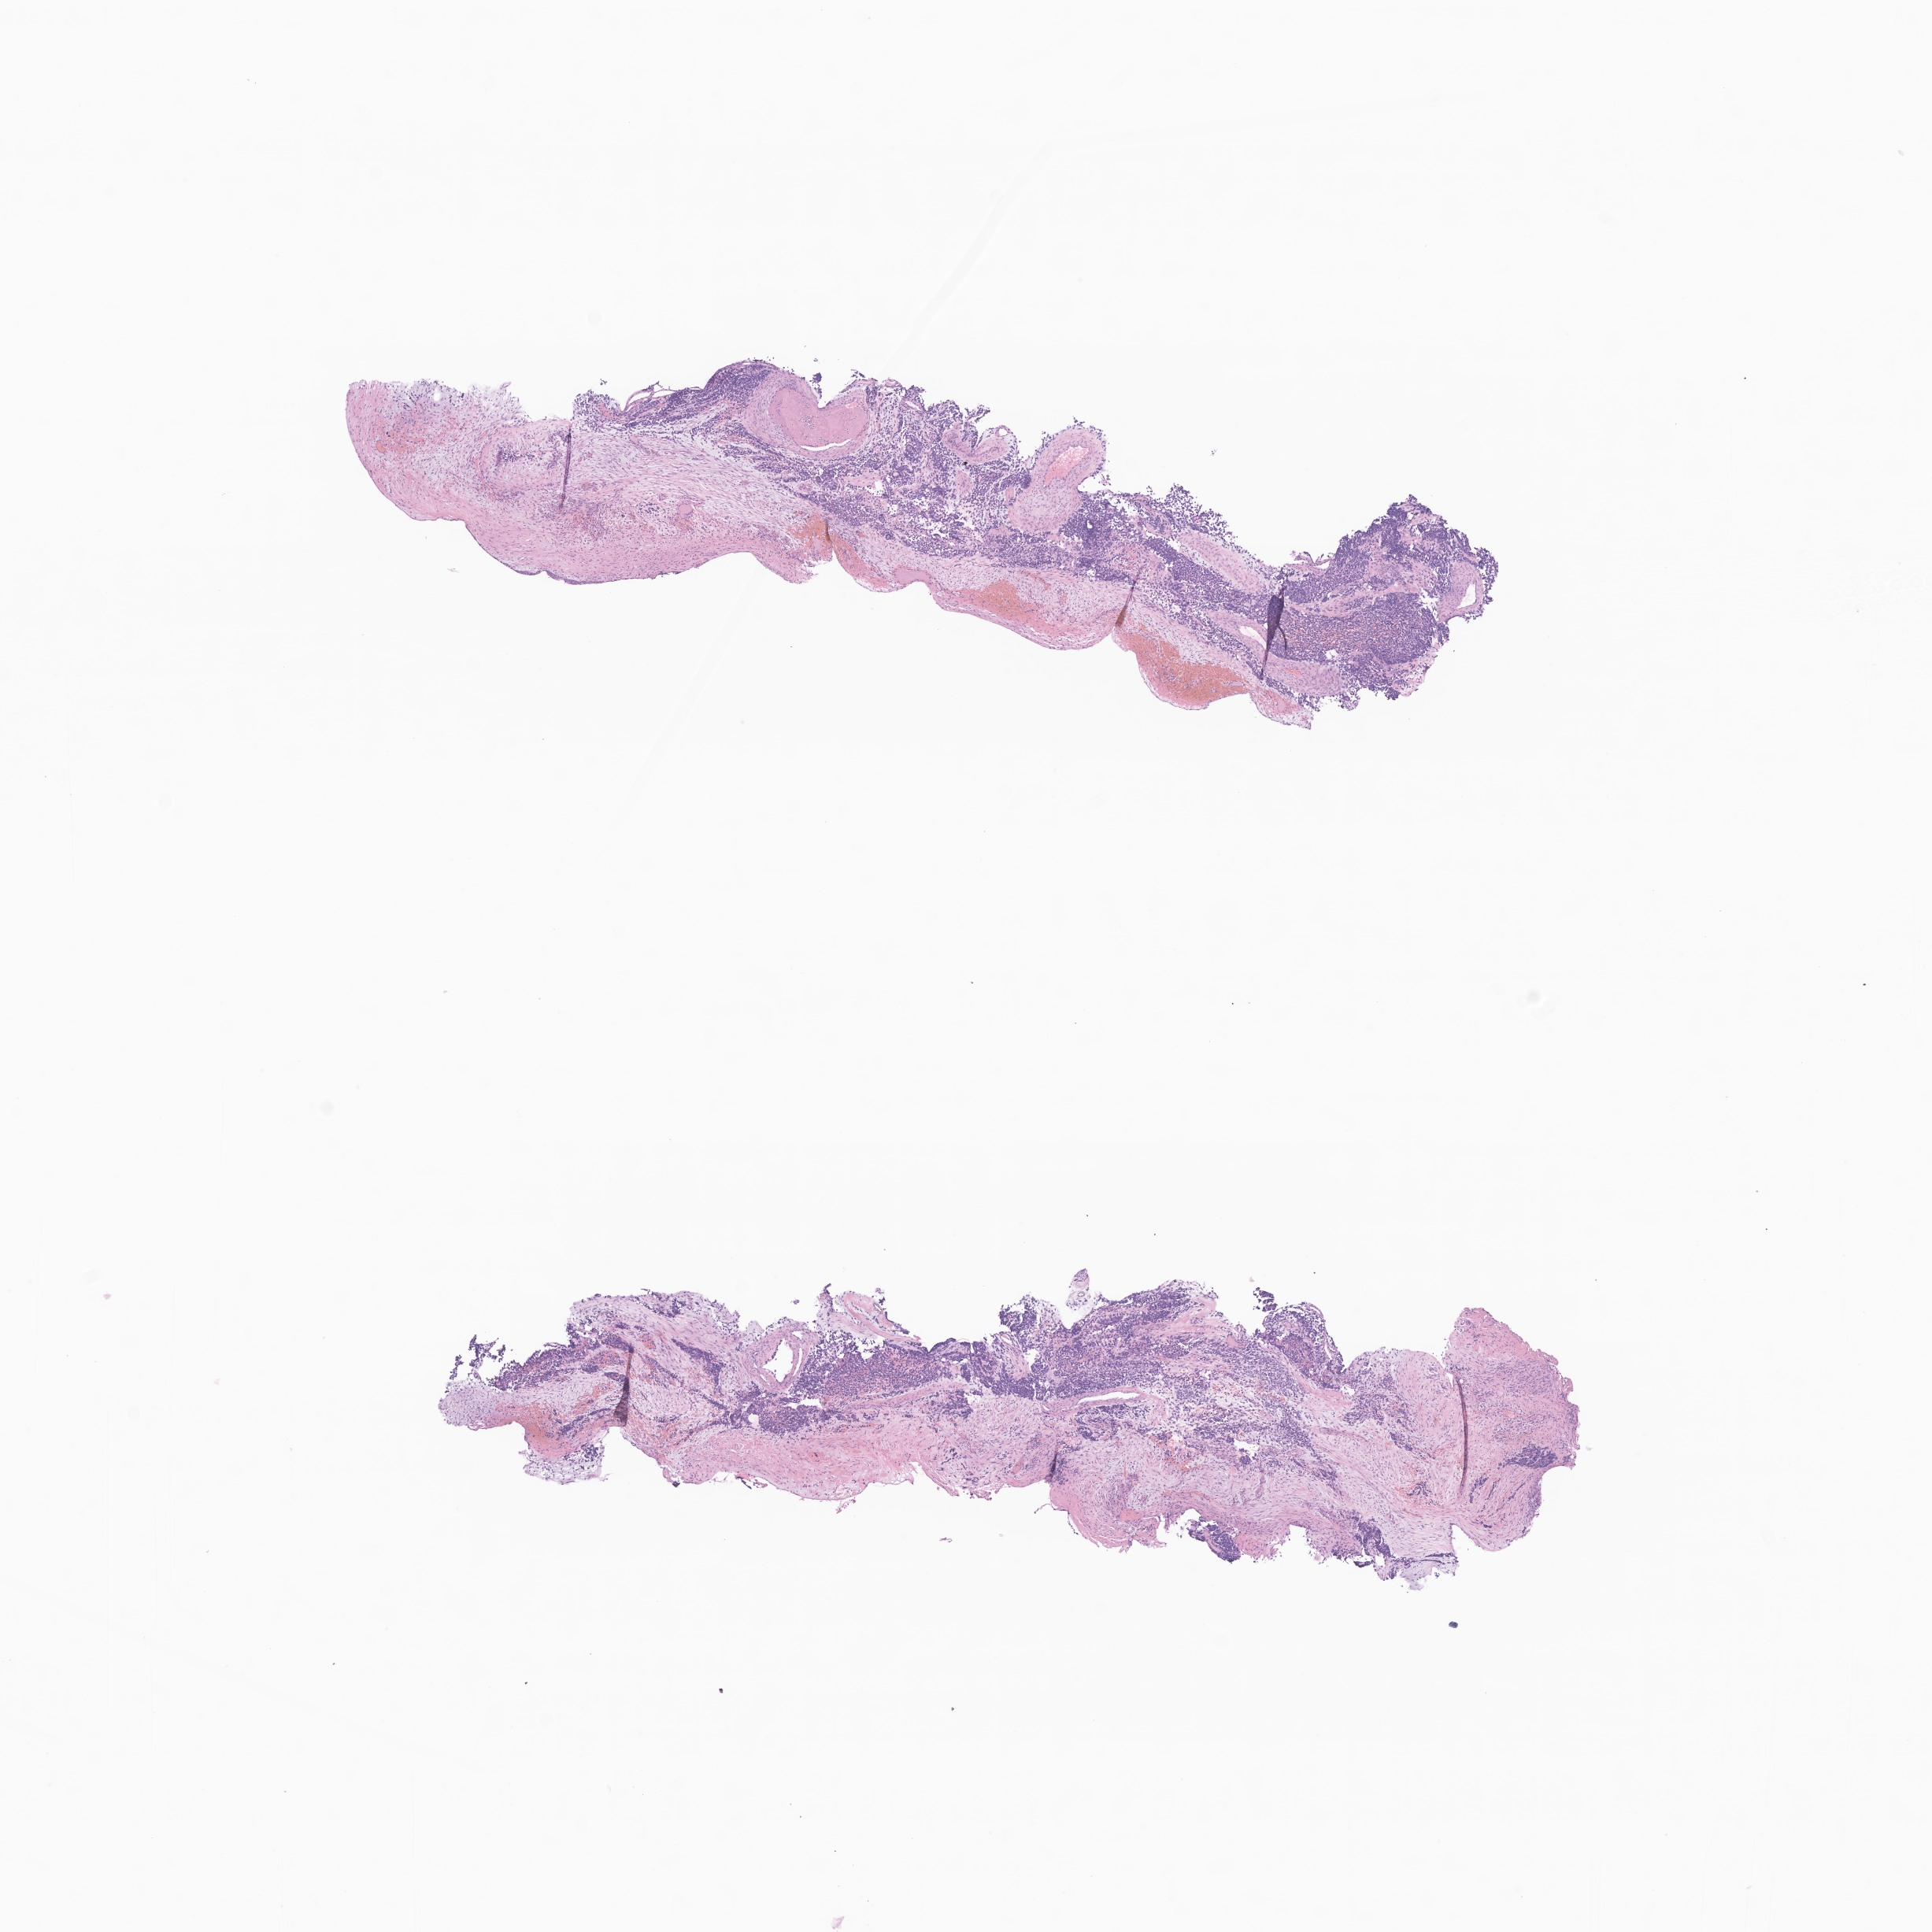
Whole-slide image, H&E stain of tumor tissue from the head and neck, low-resolution overview of the scanned area, about 10.3 x 10.3 mm. Formalin-fixed paraffin-embedded section. Patient: male, age 198 months (16 years 6 months).
Diagnosis: Alveolar rhabdomyosarcoma.